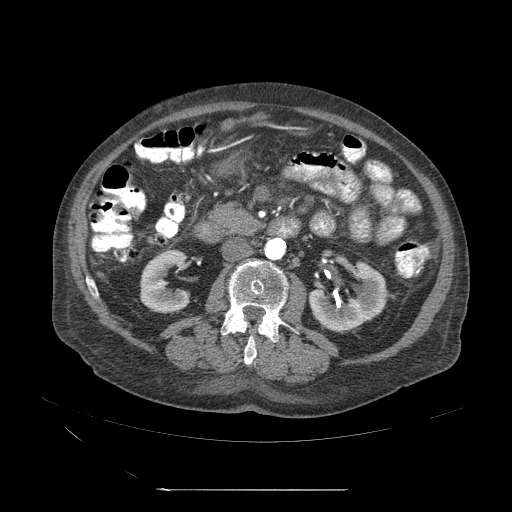
Contrast-enhanced abdominal CT (liver protocol), one axial slice; position 3 of 71 along the scan axis; reconstruction kernel STANDARD; 120 kVp; soft-tissue window (W 400 / L 40 HU); 512 × 512 image matrix. From the clinical record (not read from this slice): diagnosis: hepatocellular carcinoma (patient treated with transarterial chemoembolisation; whether this scan precedes or follows treatment is not stated here); TNM stage (as recorded): Stage-II.
Annotated regions visible in this slice (semi-automatically segmented with operator editing):
- abdominal aorta: box from (x=264, y=238) to (x=286, y=262) px